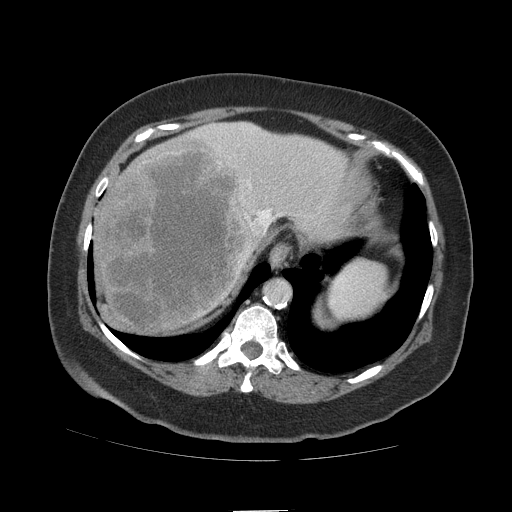
Contrast-enhanced abdominal CT (liver protocol), one axial slice. Position 87 of 109 along the scan axis. 140 kVp. Soft-tissue window (W 400 / L 40 HU). 2.5 mm slice thickness. 512 × 512 image matrix, field of view 420 × 420 mm. From the clinical record (not read from this slice): diagnosis: hepatocellular carcinoma (patient treated with transarterial chemoembolisation; whether this scan precedes or follows treatment is not stated here); TNM stage (as recorded): Stage-IVB; Child-Pugh class: A; tumour differentiation: poorly differentiated.
Structures marked on this image (semi-automatically segmented with operator editing):
- abdominal aorta: bounding box [x1, y1, x2, y2] px = [265, 281, 290, 305]
- liver parenchyma outside the tumour (the mass and vessels are separate outlines, so this box may not span the whole liver): [94, 122, 368, 332]
- mass: [95, 134, 258, 331]
- liver vessels: [197, 124, 282, 234]